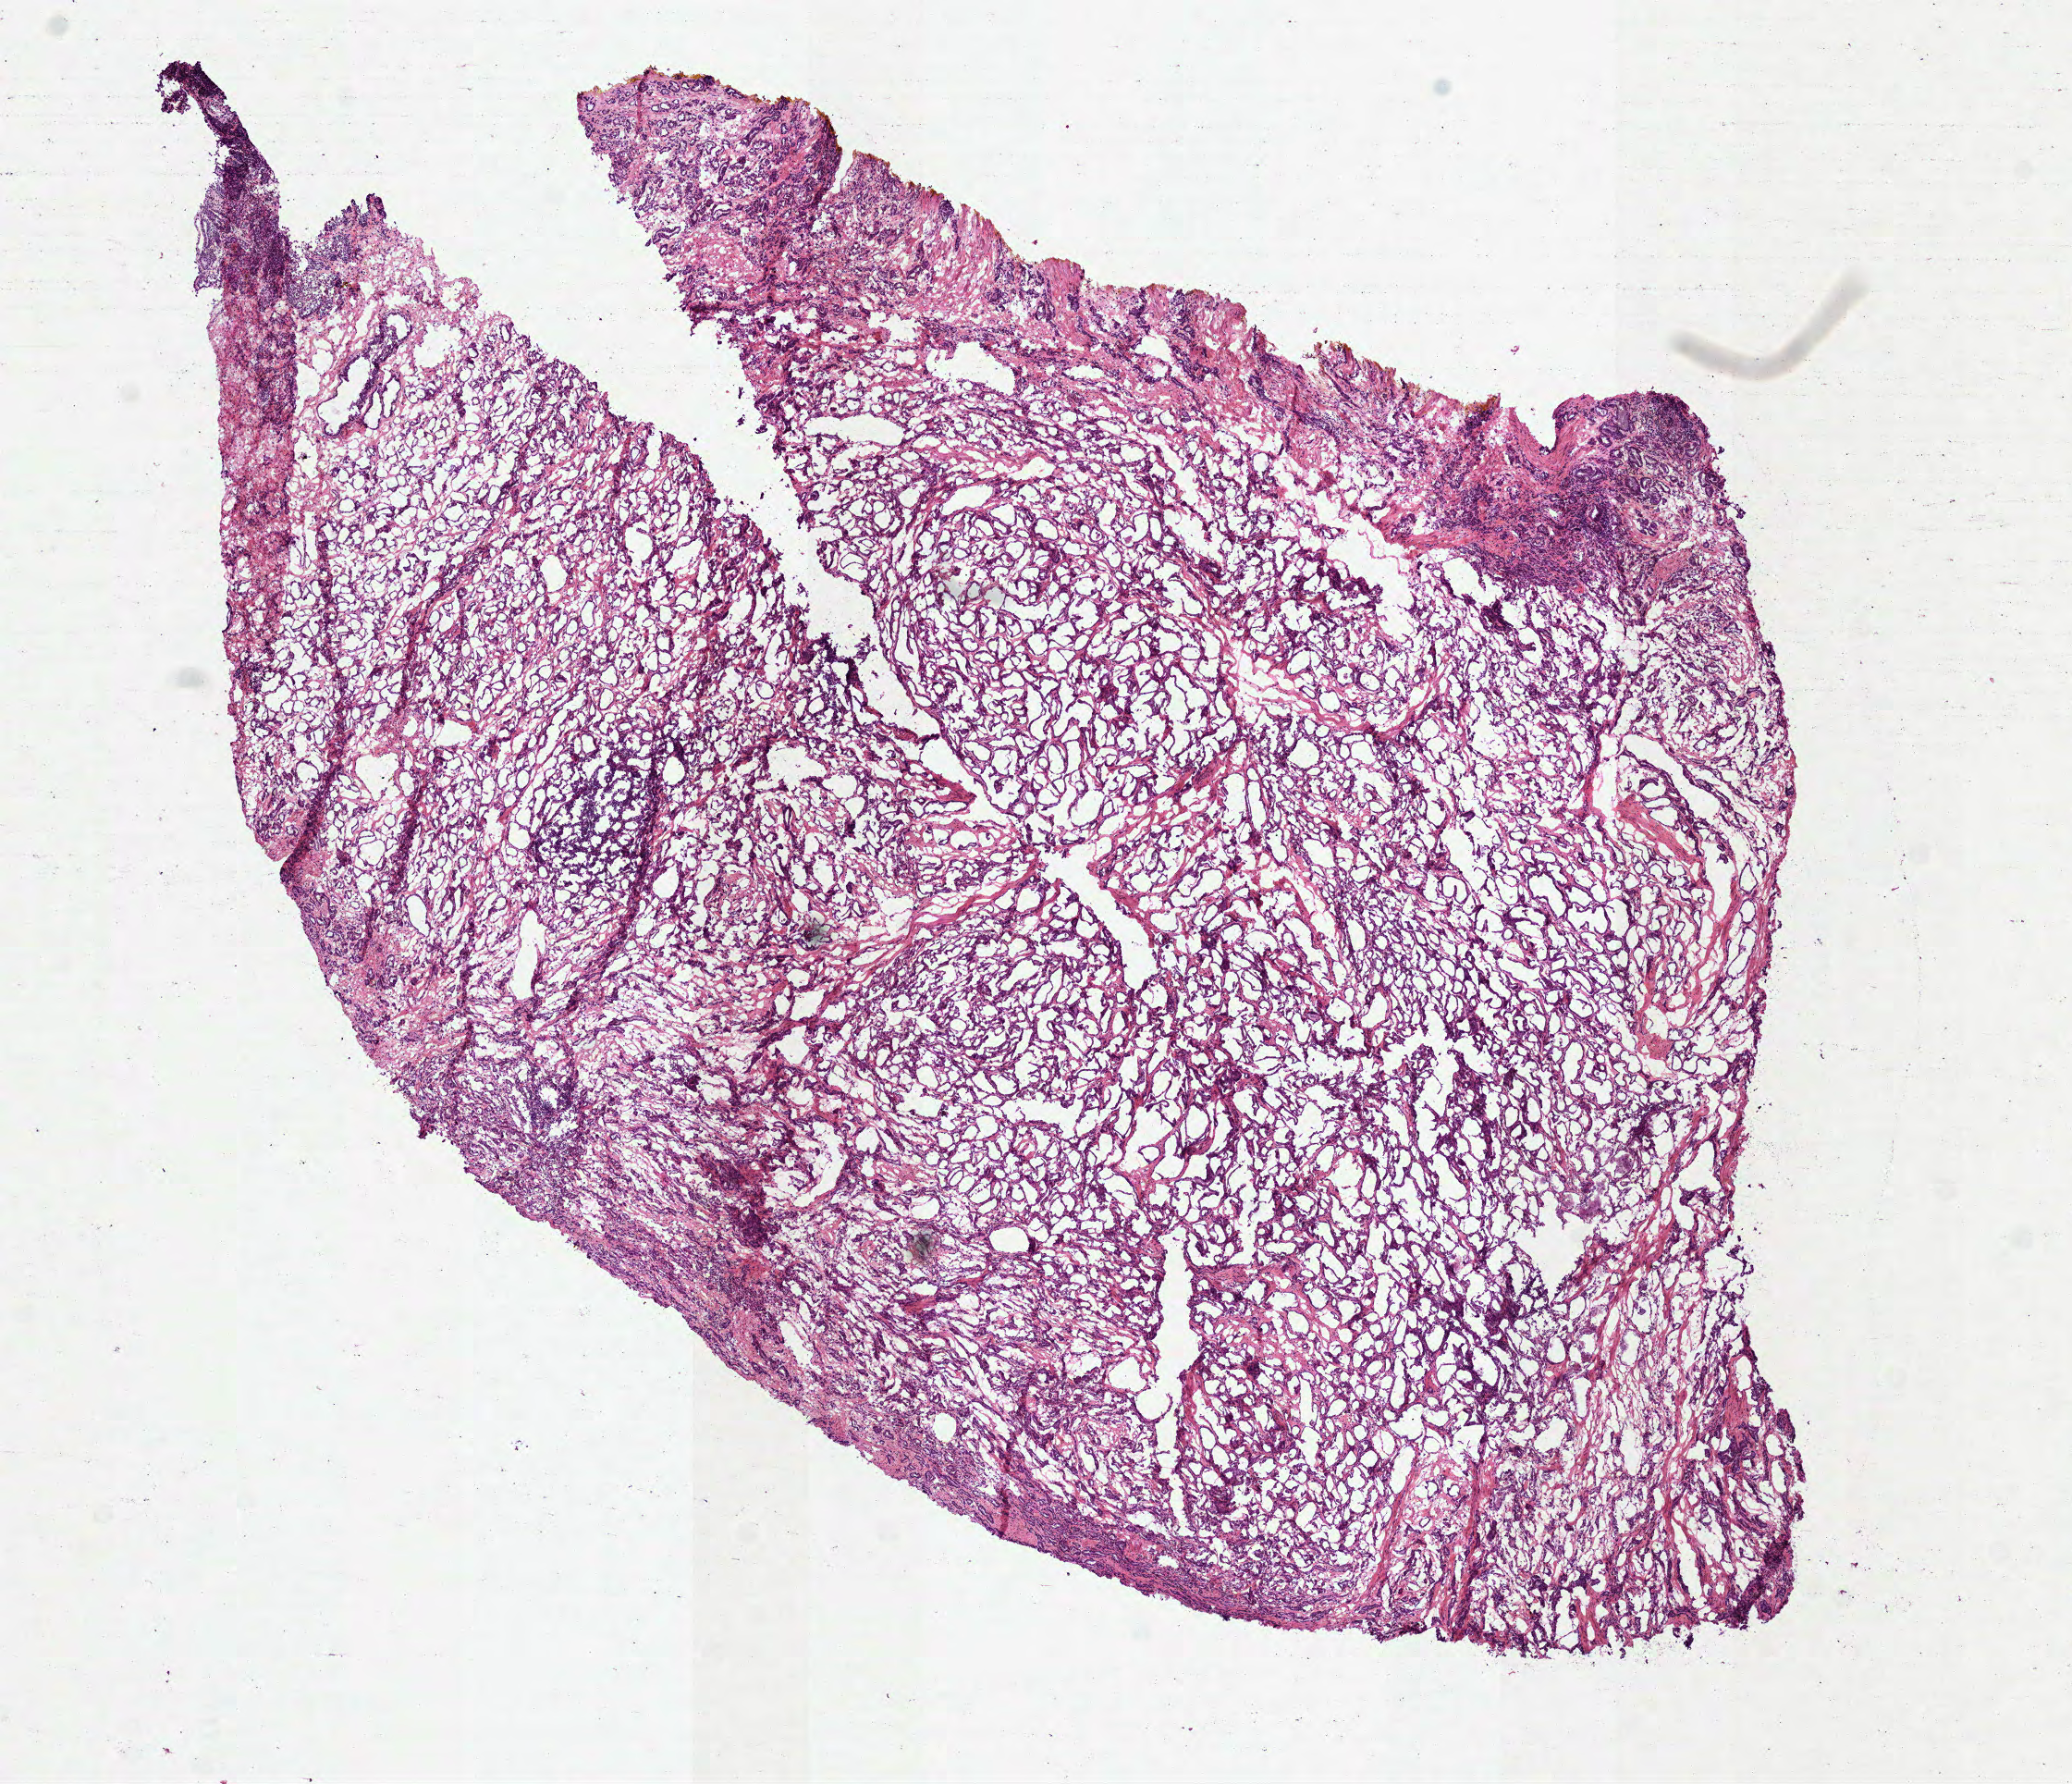
Hematoxylin and eosin (H&E) stained whole-slide image — a low-resolution overview of the entire scanned area, about 9.0 x 7.8 mm (from a 40x scan); frozen section from the top of the tissue portion; sample: primary tumour, prostate. Male patient; age at initial diagnosis 53 years.
Diagnosis: Acinar cell carcinoma (prostate gland).